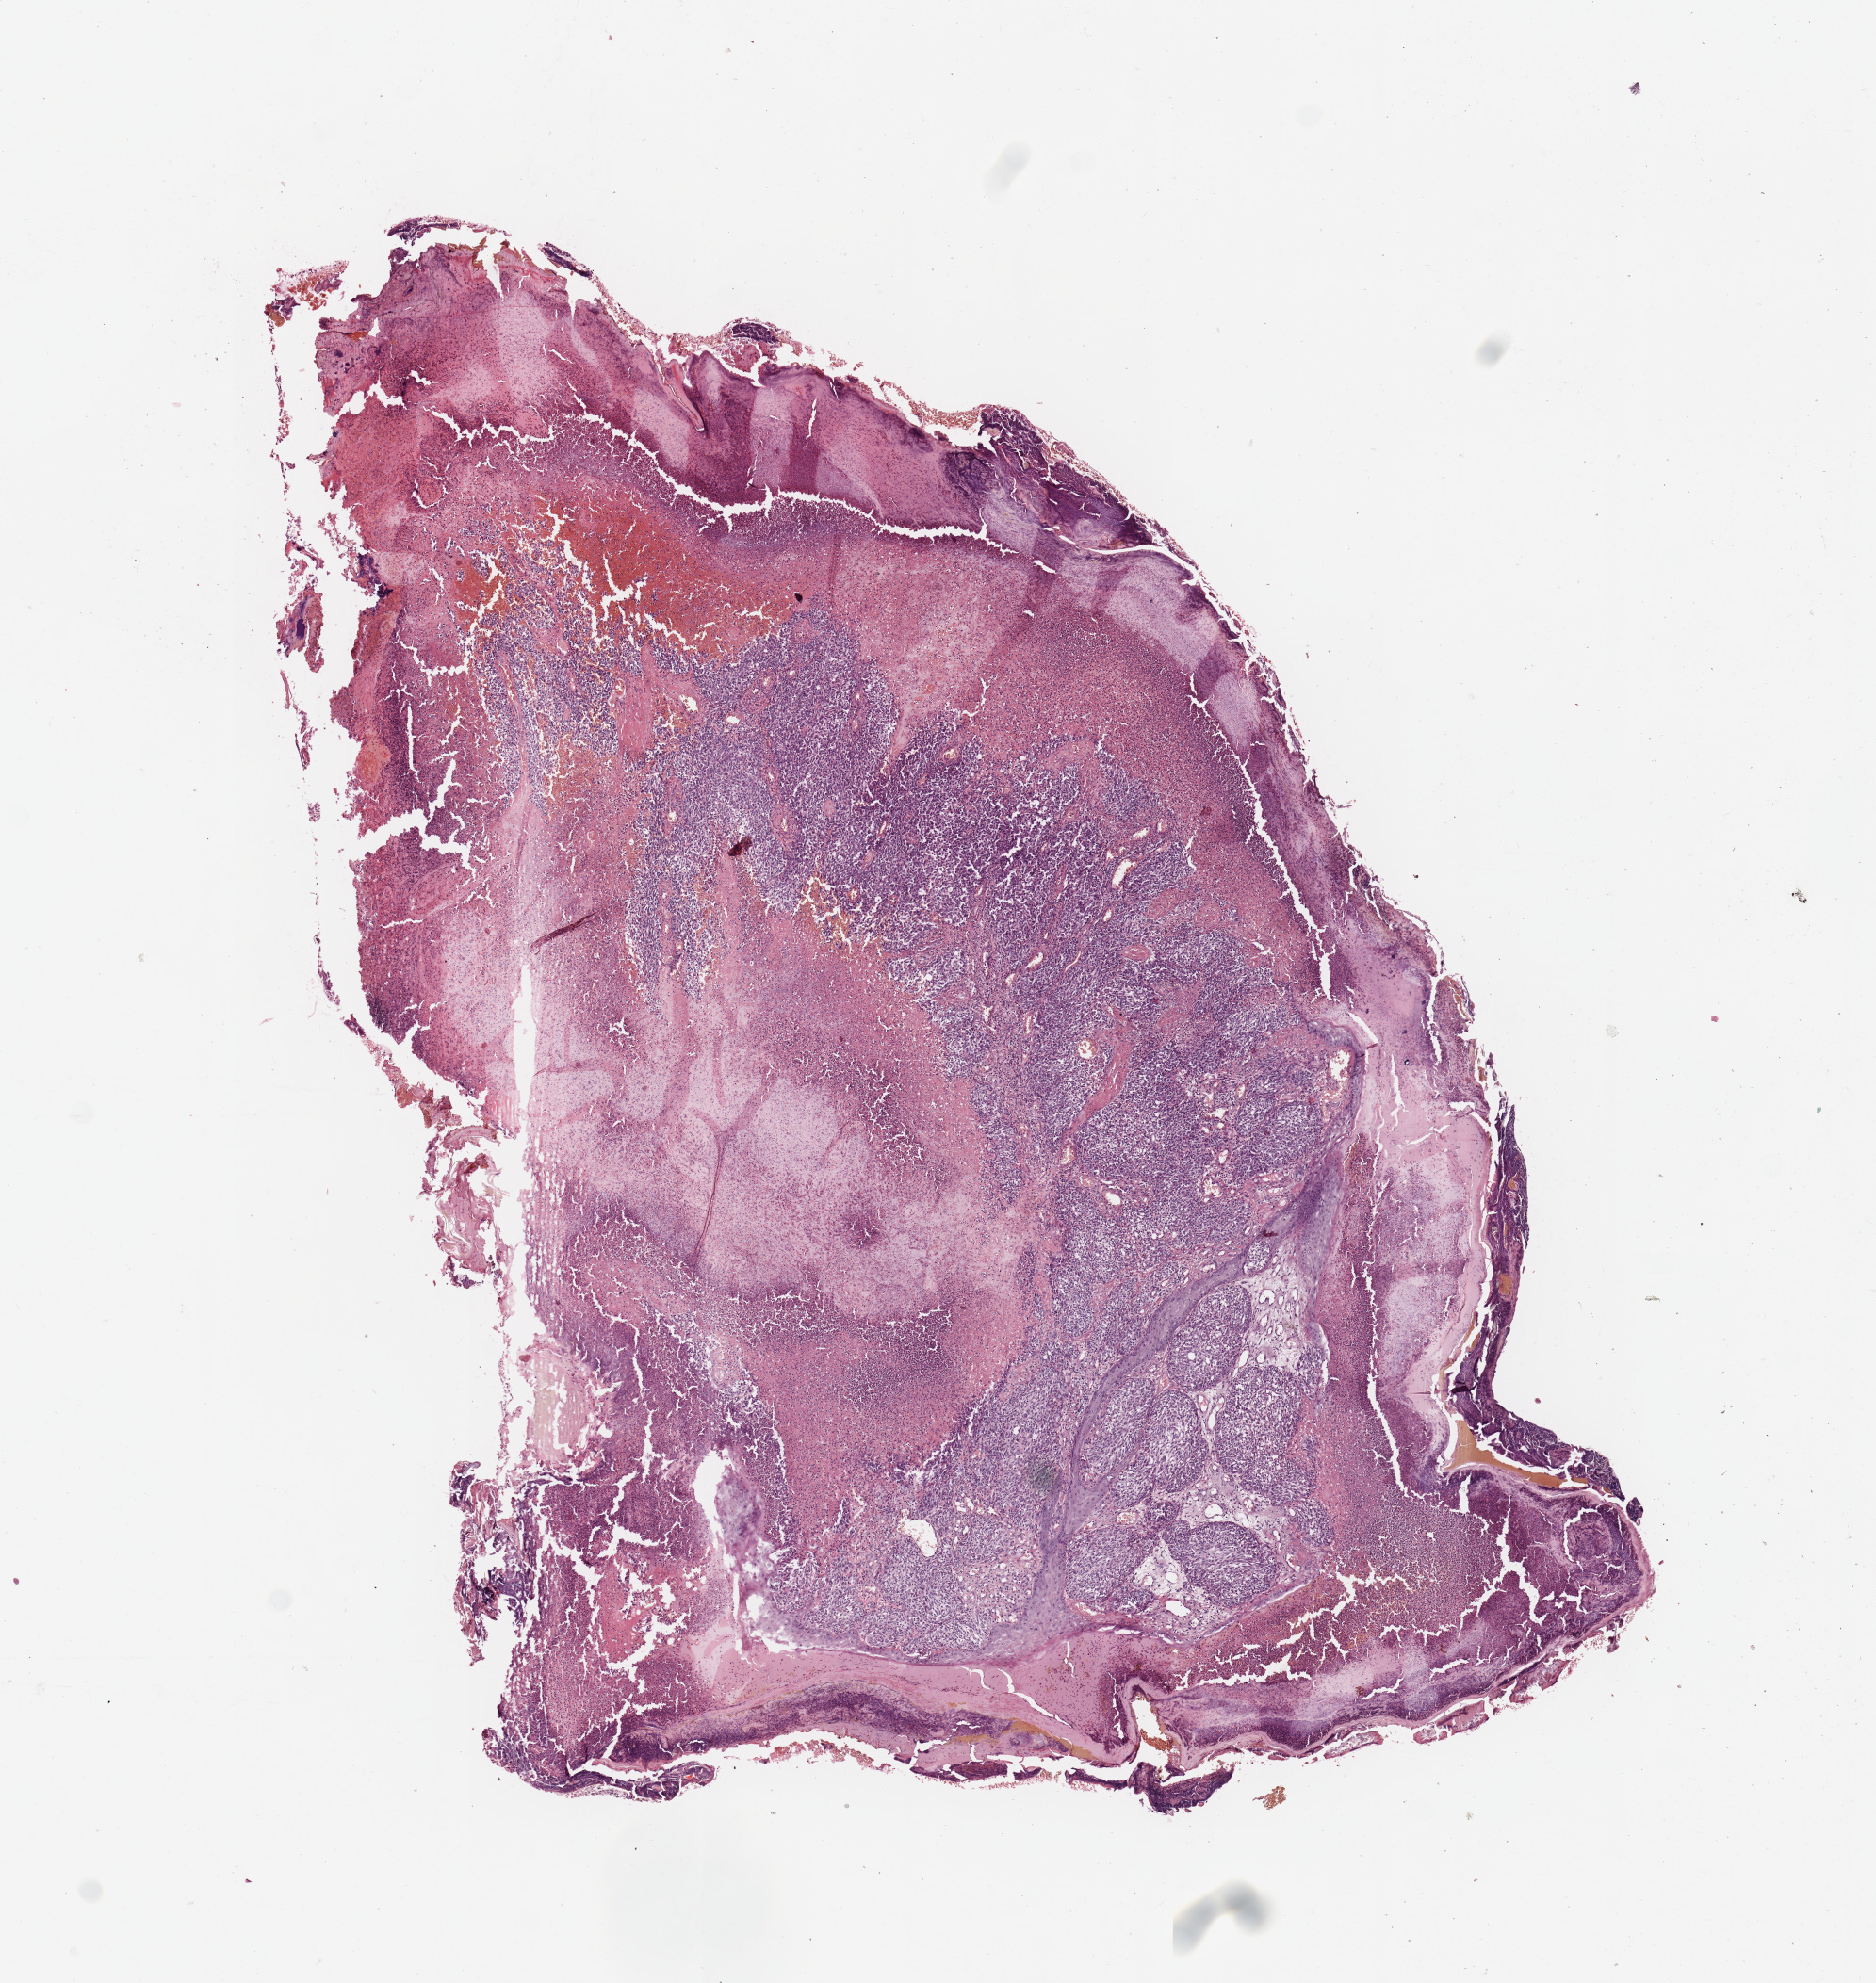
Whole-slide histology image, H&E, shown as a low-resolution overview of the whole scanned area (about 7.9 x 8.3 mm), tumour tissue sample, sampled site: trunk. 73-year-old male patient. Pathologist review of this section (percent, as recorded): tumour nuclei 80%, necrosis 5%.
AJCC pathologic stage: IIC. Primary tumour site (as recorded): trunk. Diagnosis: Malignant melanoma, NOS.